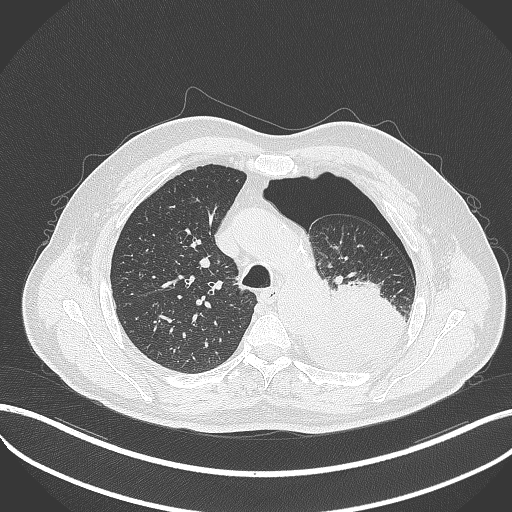
Chest CT, one axial slice; slice 373 of 464 in the series (ordered by position); lung window (W 1500 / L -600 HU); 512 × 512 image matrix, field of view 400 × 400 mm. Patient: male, 76 years. From the clinical record (not read from this slice): clinical TNM (as recorded): T3 N0 M1b.
Outlined on this slice (bounding box drawn by a radiologist):
- lung tumour (recorded histology: adenocarcinoma): bounding box [x1, y1, x2, y2] px = [288, 271, 411, 371]